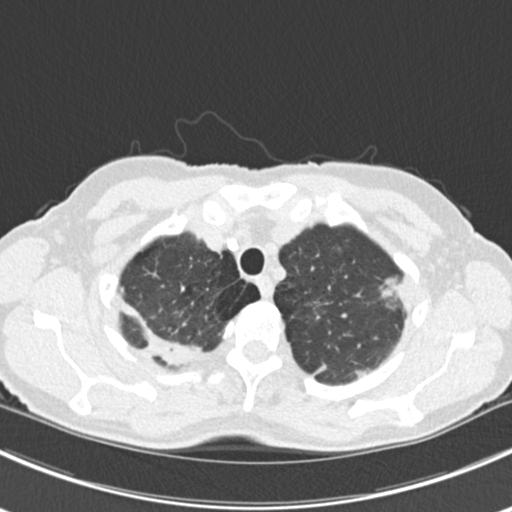
Axial slice from a low-dose chest CT screening exam. Baseline annual screen. Lung window (W 1500 / L -600 HU). Slice 31 of 224 in the series. Female participant, aged 63 years at enrolment. Current smoker at enrolment.
Expert-annotated lung lesion, box from (x=367, y=267) to (x=419, y=320) px. The screening reader recorded 10 non-calcified nodules or masses ≥4 mm on this exam (right lower lobe, right lower lobe, left lower lobe, left lower lobe, right middle lobe, right lower lobe, left lower lobe, left upper lobe, right upper lobe, left upper lobe); which of them this box marks is not recorded. Official screen result: positive, change unspecified: nodule(s) >= 4 mm or enlarging nodule(s), mass(es), or other non-specific abnormalities suspicious for lung cancer. Later outcome: lung cancer diagnosed 751 days after this screen (after the third annual screen) — bronchiolo-alveolar adenocarcinoma, NOS, right upper lobe, right middle lobe, right lower lobe, left upper lobe, left lower lobe, moderately differentiated (G2), stage IV (AJCC 6th edition).